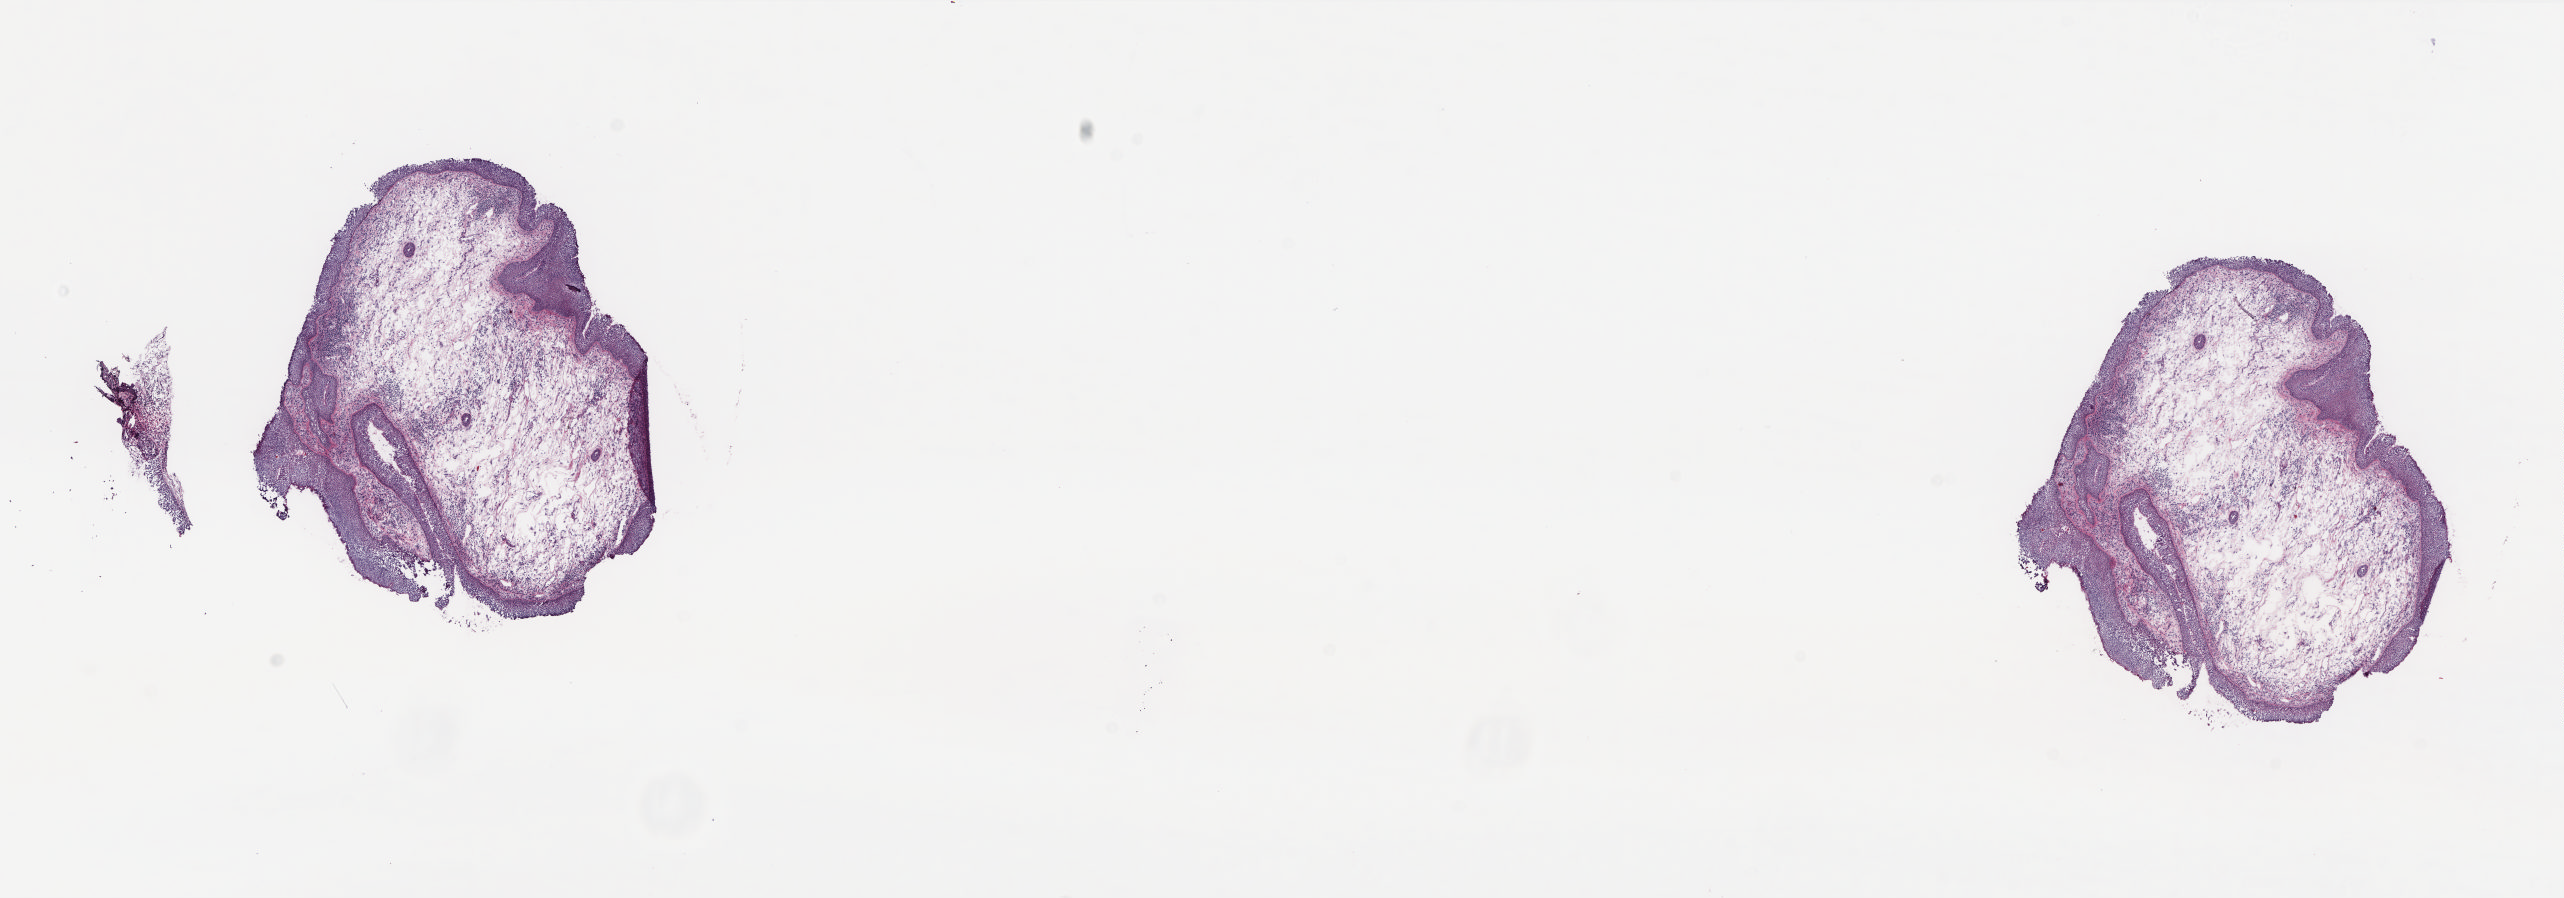
Whole-slide histology image, Hematoxylin and eosin (H&E) stained, low-resolution overview of the scanned area, about 20.7 x 7.2 mm (acquisition: 20x scan). Frozen section. Sample: solid tissue normal (non-tumour tissue), head and neck. Patient: male, age at initial diagnosis 65 years. Slide review estimates, as recorded: tumour cells 0%, tumour nuclei 0%, normal cells 70%, stromal cells 30%, necrosis 0%. Infiltration values recorded for this section: lymphocyte infiltration 40%, monocyte infiltration 20%, neutrophil infiltration 20%.
This section: solid tissue normal sample (biorepository sample class). Patient diagnosis: Squamous cell carcinoma, keratinizing, NOS (larynx, NOS).